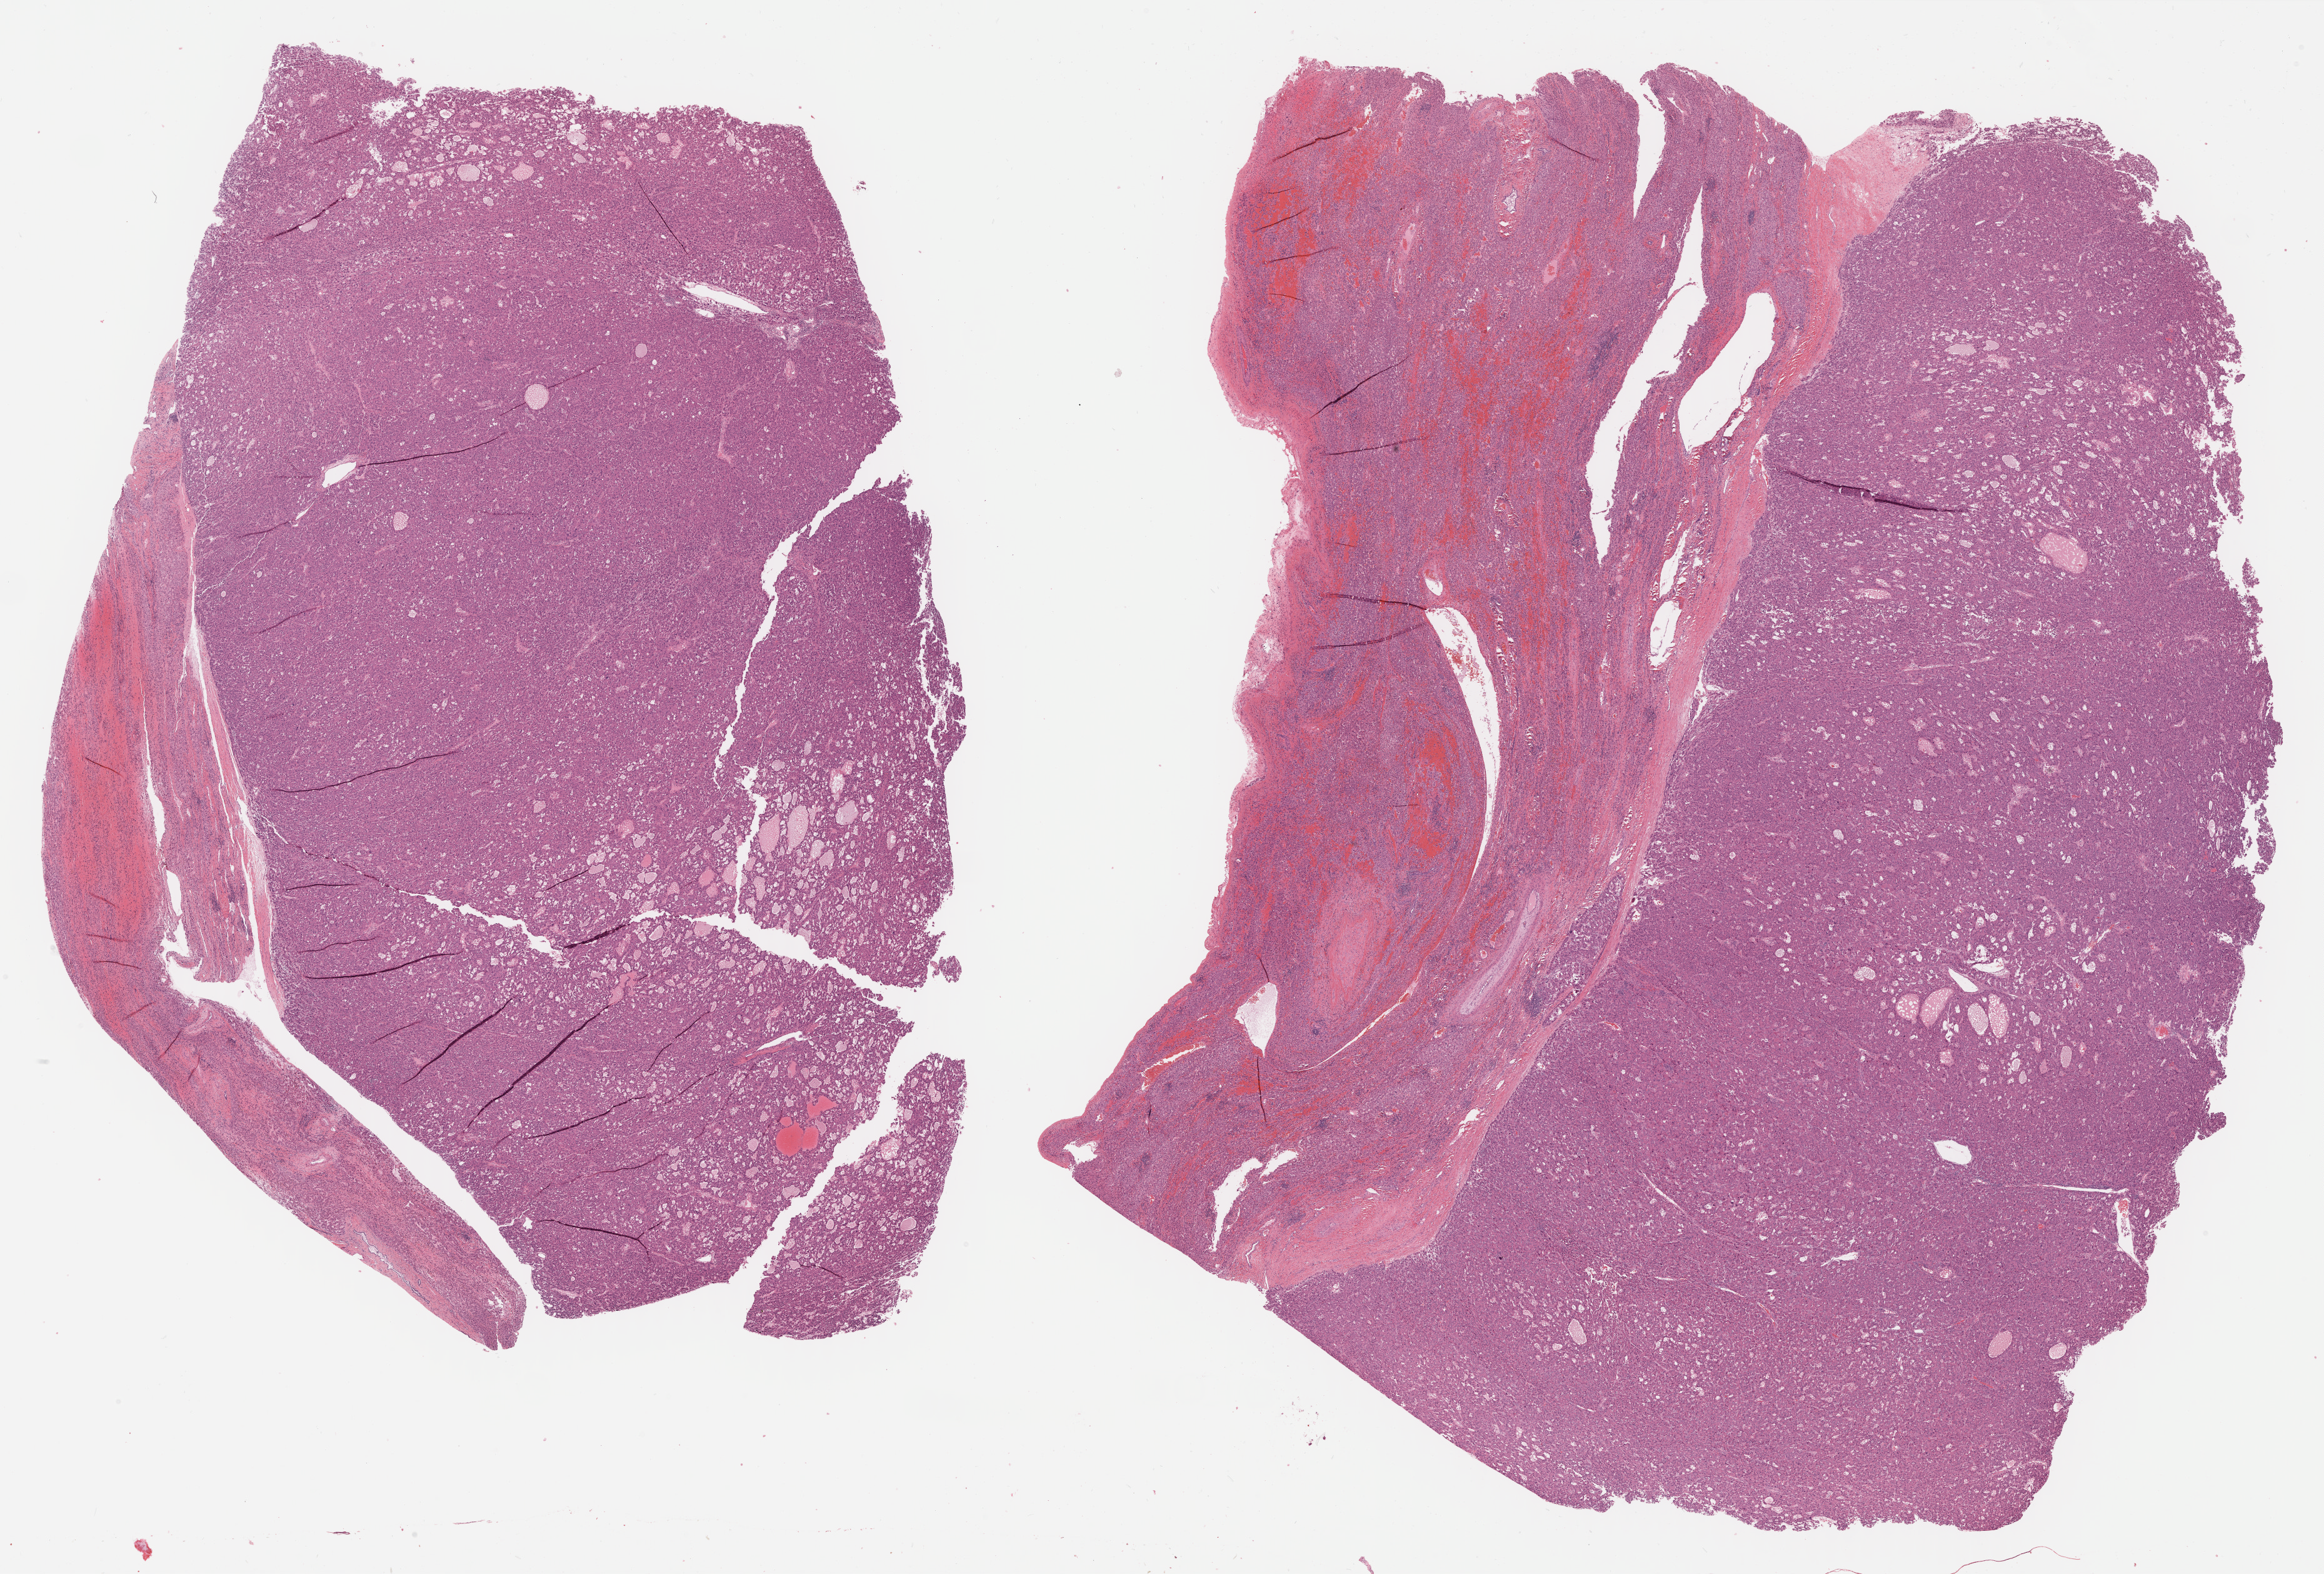
Whole-slide histology image, Hematoxylin and eosin (H&E) stained — shown as a low-resolution overview of the whole scanned area (about 30.1 x 20.4 mm, acquisition: 40x scan); formalin-fixed paraffin-embedded (FFPE) diagnostic section; primary tumour sample from the liver. Patient: male, age at initial diagnosis 69 years.
Diagnosis: Hepatocellular carcinoma, NOS.